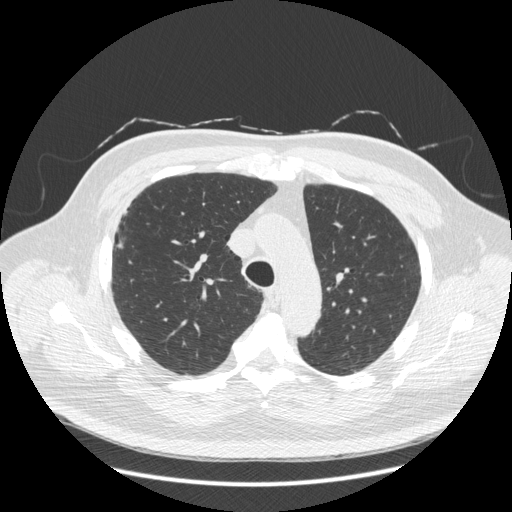
Axial slice from a low-dose chest CT screening exam. Second annual screen. Lung window (W 1500 / L -600 HU). Standard (soft-tissue) reconstruction kernel (STANDARD). 120 kVp. Slice 72 of 281 in the series. 512 × 512 image matrix, field of view 400 × 400 mm. Male, age 66 years at enrolment.
- Expert reader's lesion annotation, box from (x=101, y=212) to (x=143, y=262) px.
- The screening reader recorded 2 non-calcified nodules or masses ≥4 mm on this exam (right lower lobe, right lower lobe); which of them this box marks is not recorded.
- Official screen result: positive, other.
- Later outcome: lung cancer diagnosed 403 days after this screen — non-small cell carcinoma, right upper lobe, stage IV (AJCC 6th edition), 50 mm at pathology.